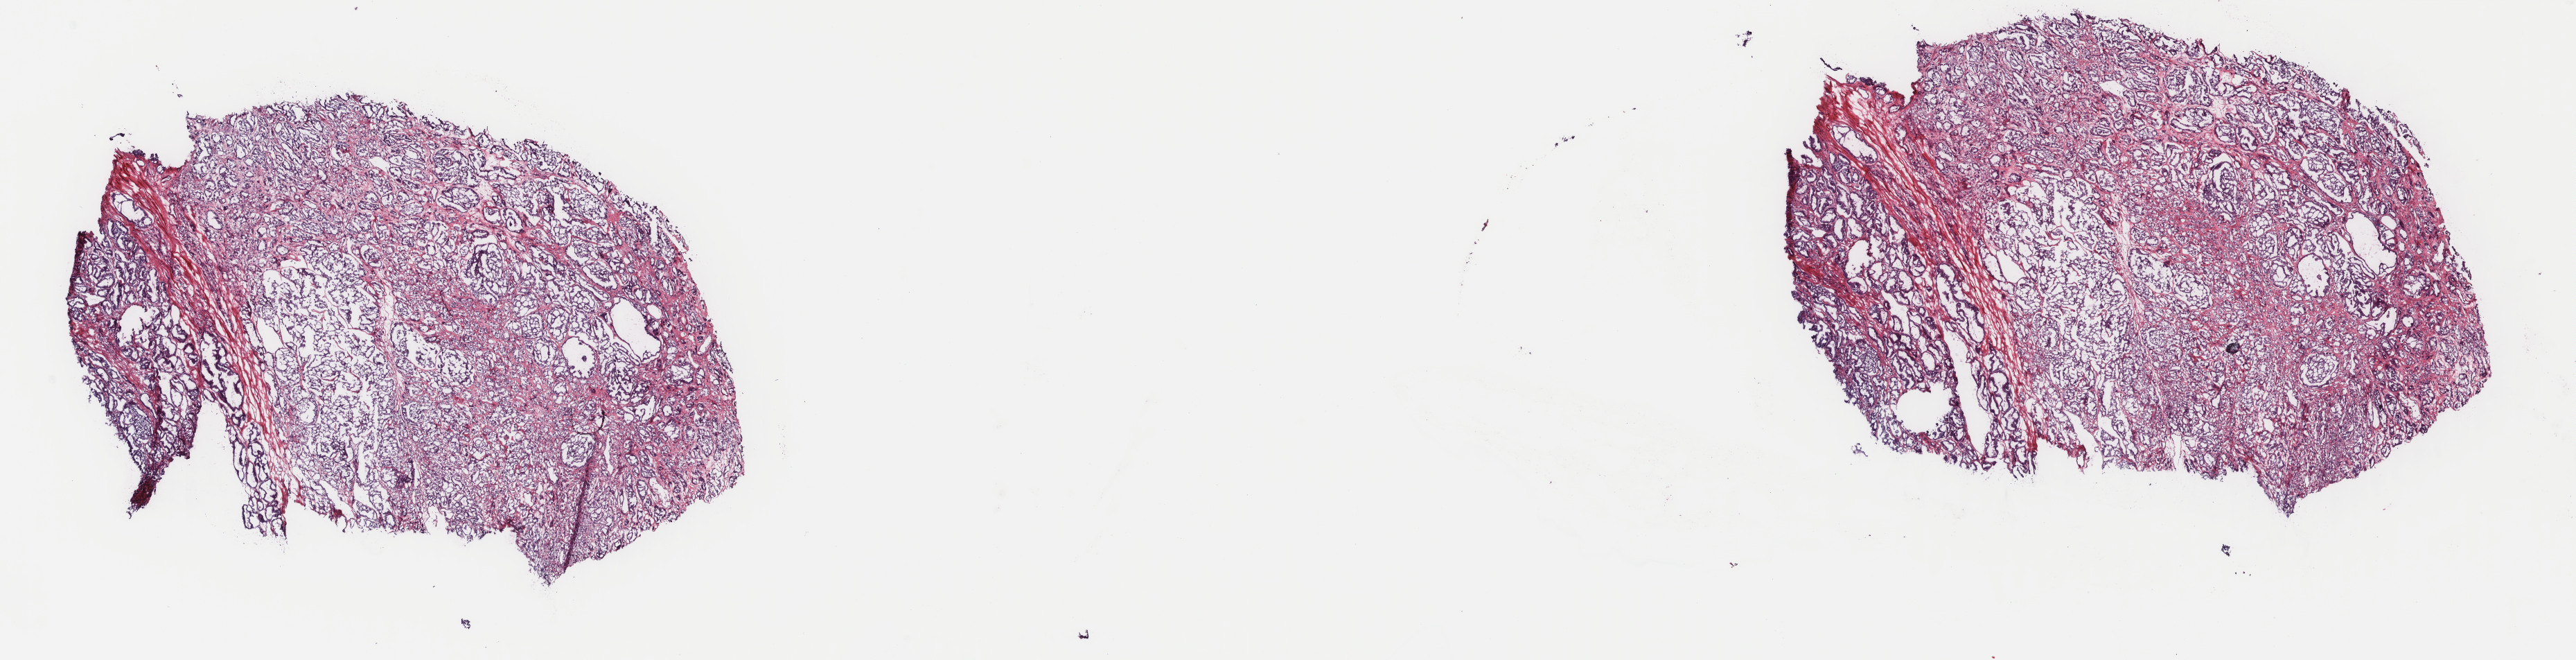
Digitized H&E tissue section (whole slide), whole scanned area (about 29.5 x 7.6 mm) shown as a low-resolution overview; frozen section from the top of the tissue portion; prostate, primary tumour sample. Patient: male, age at initial diagnosis 68 years. Gleason score: 9 (4+5). Pathologist review of this section (percent, as recorded): tumour cells 100%, tumour nuclei 80%, normal cells 0%, stromal cells 0%, necrosis 0%. Infiltration values recorded for this section: lymphocyte infiltration 1%, monocyte infiltration 0%, neutrophil infiltration 0%.
Histologic diagnosis: Adenocarcinoma, NOS (prostate gland). Laterality: bilateral.